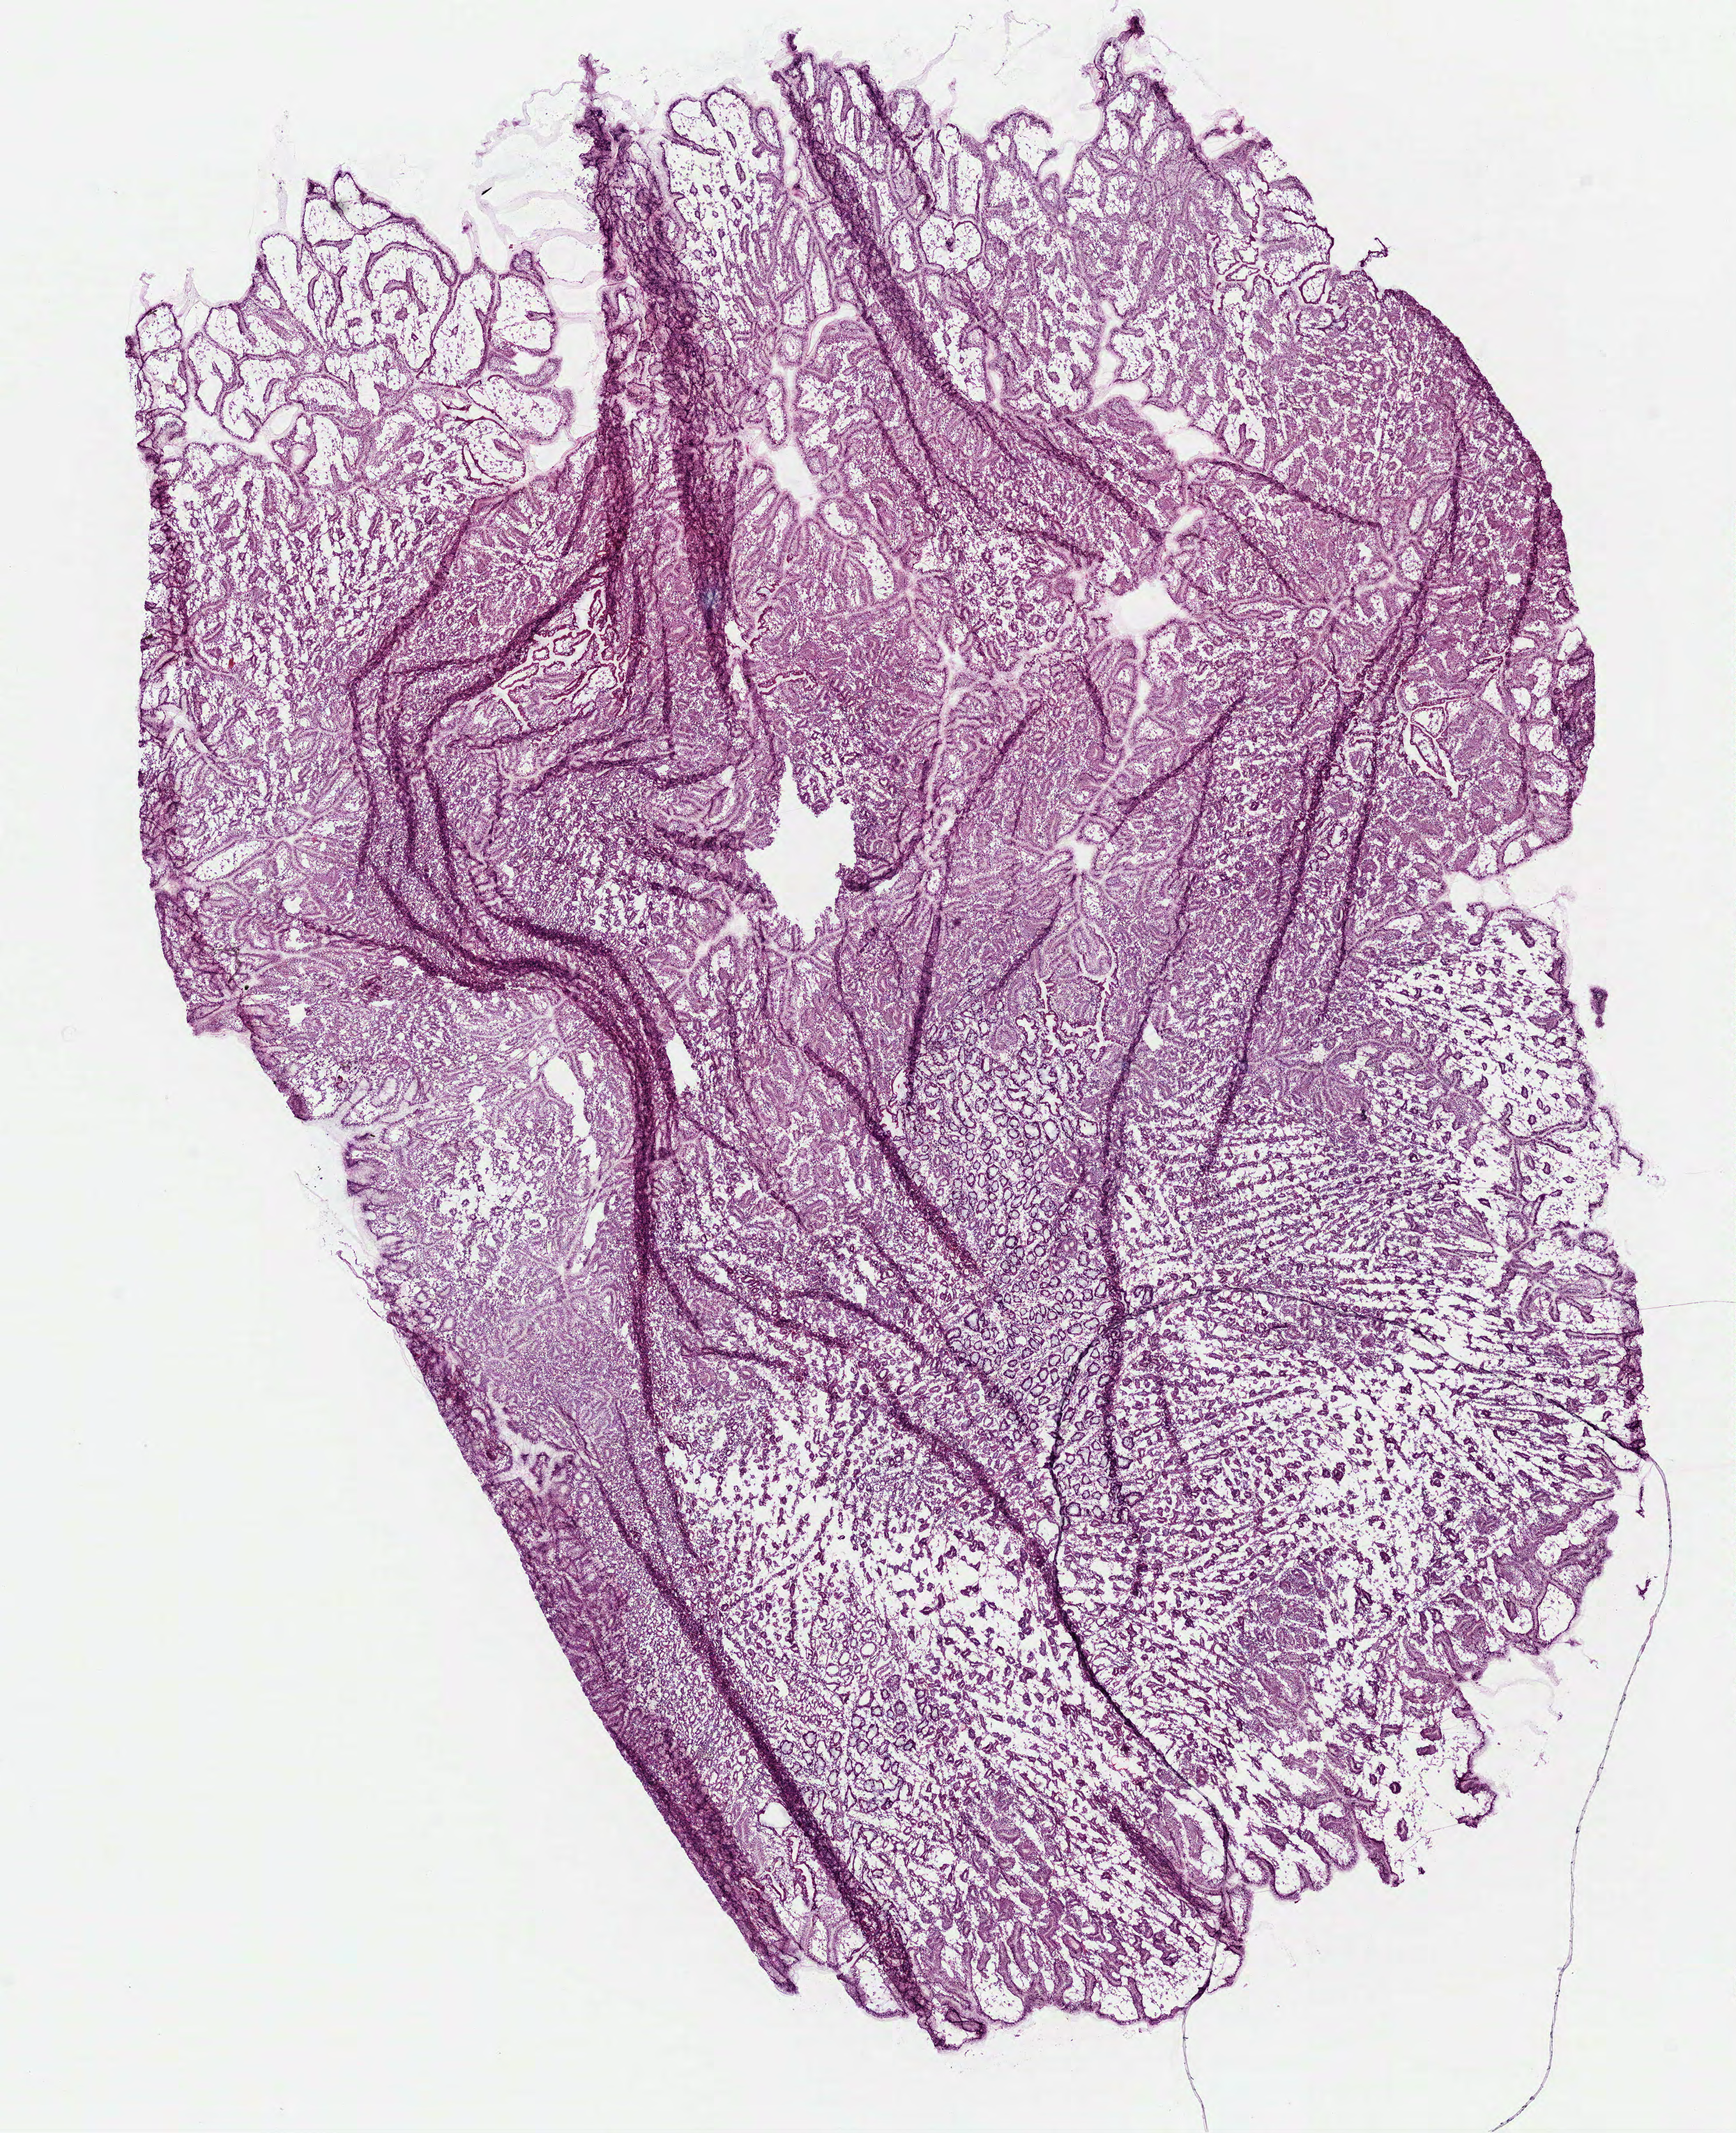
H&E whole-slide image, shown as a low-resolution overview of the whole scanned area (about 10.0 x 12.3 mm, acquisition: 40x scan), frozen section, solid tissue normal (non-tumour tissue) sample from the stomach. Patient: female, age at initial diagnosis 57 years.
This section: solid tissue normal sample (biorepository sample class). Patient diagnosis: Adenocarcinoma, NOS.